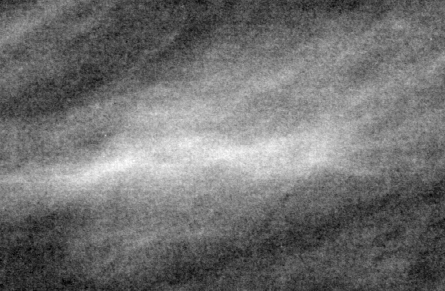
Crop from a digitized film mammogram around one marked abnormality, right breast, MLO view.
Mass, shape round, margins circumscribed; BI-RADS assessment category 2; subtlety rating 5 on a 1 (subtle) to 5 (obvious) scale; pathology result (as recorded, not read from the image): benign.